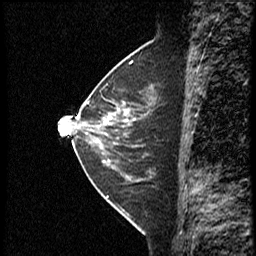
Breast MRI (dynamic contrast-enhanced), one sagittal slice; slice 17 of 40 in the series (ordered by position); dynamic contrast-enhanced study with each time point stored as its own series, time point 2 of 4 at this slice position (early post-contrast, ordered by acquisition time); 1.5 T; TE 4.2 ms, TR 18.8 ms; 3 mm slice thickness; 256 × 256 image matrix, field of view 200 × 200 mm. Female patient. From the clinical record (not read from this slice): setting: breast cancer imaged before/during neoadjuvant chemotherapy; receptor status: HER2-positive.
Annotated regions visible in this slice (semi-automatic segmentation, software-assisted and operator-edited):
- analysis volume of interest (the breast-tissue region the enhancement analysis was run in; not a lesion): bounding box <91,79,162,153> (left, top, right, bottom; pixels)
- tumour enhancement mask (voxels above the 100 % enhancement threshold inside the analysis volume of interest): <103,108,132,124>